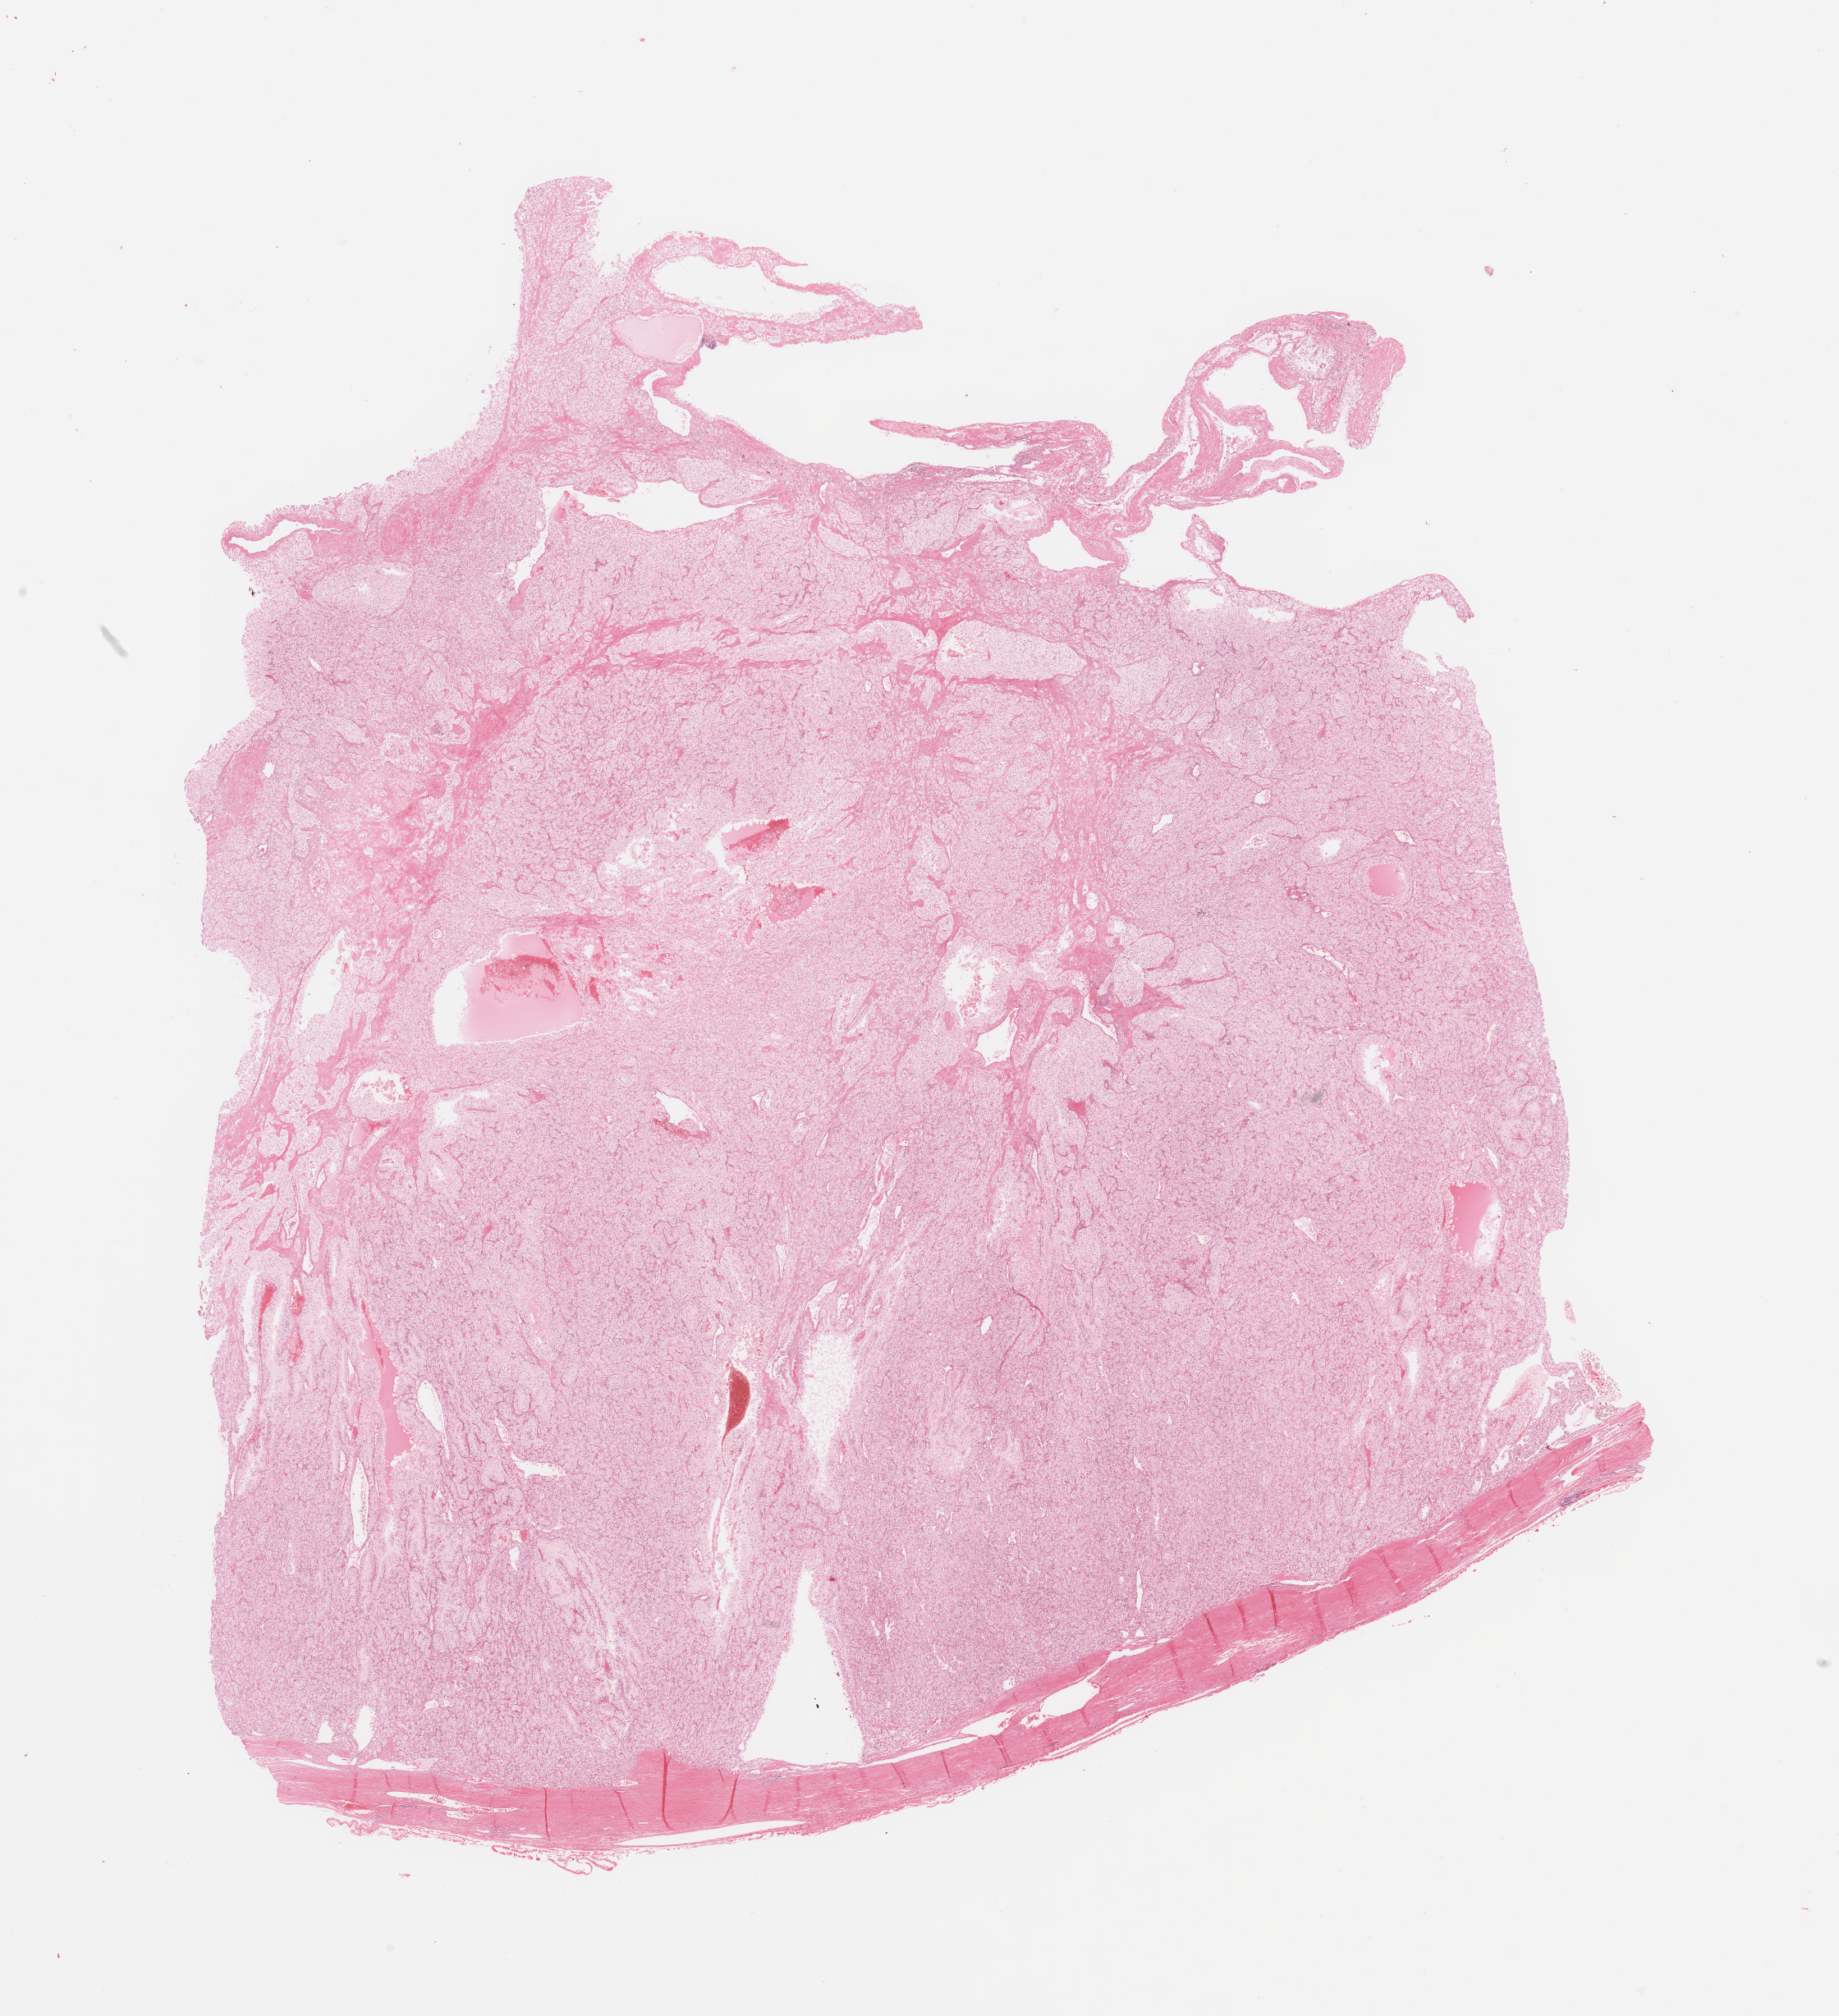
Digitized Hematoxylin and eosin (H&E) stained tissue section (whole slide) — a low-resolution overview of the entire scanned area, about 17.7 x 19.4 mm, kidney, tumour tissue. Patient: male, age 51 years. Histologic grade: G2 (moderately differentiated).
Histologic diagnosis: Renal cell carcinoma, NOS.